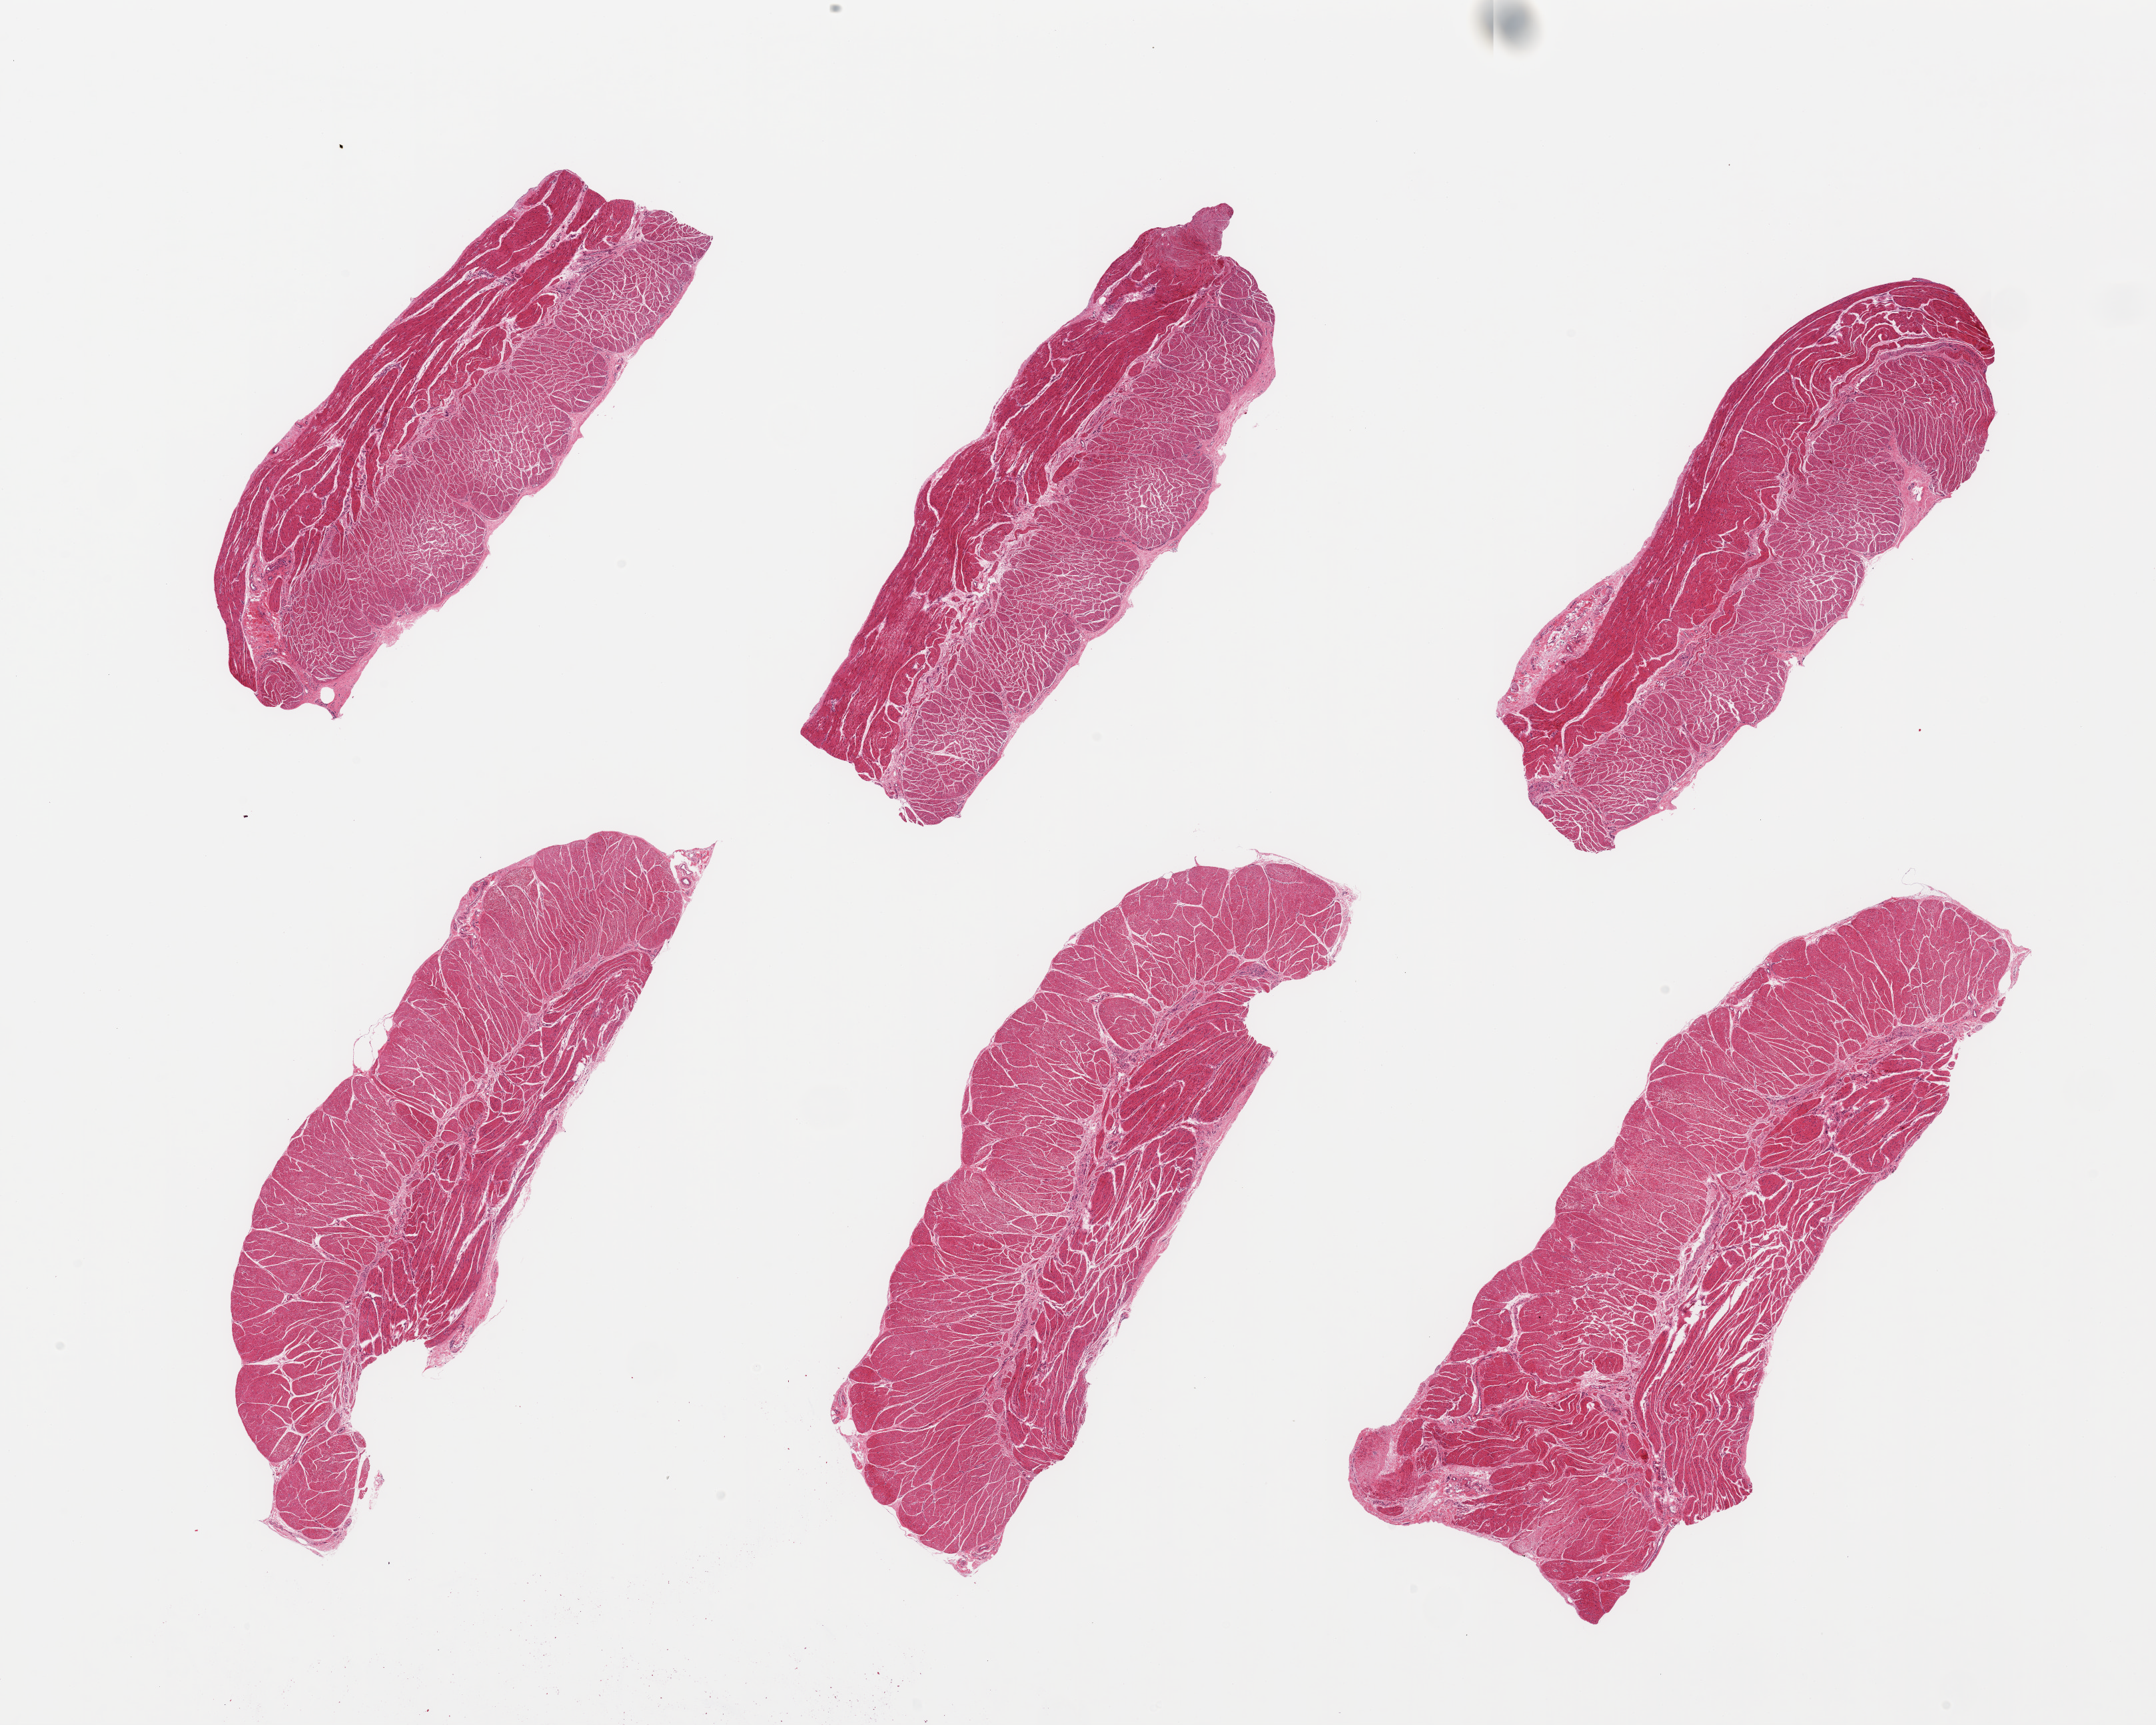
Whole-slide image, H&E stain — shown as a low-resolution overview of the whole scanned area (about 25.6 x 20.5 mm); PAXgene-fixed, paraffin-embedded tissue; target tissue: esophageal muscle; donor tissue sample.
Pathologist's review note for this sample: 6 pieces, confirmed target muscularis.